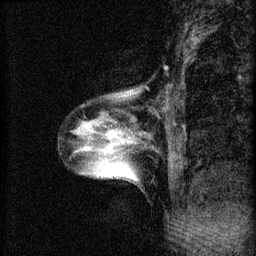
Breast MRI (dynamic contrast-enhanced), one sagittal slice. Position 14 of 60 along the scan axis. 3 images stored at this slice position (order not interpretable as contrast timing). 1.5 T. TE 4.2 ms, TR 8.2 ms. 2 mm slice thickness. 256 × 256 image matrix, field of view 180 × 180 mm. Patient: female, 40 years.
Annotated regions visible in this slice (semi-automatically segmented with operator editing):
- analysis volume of interest (the breast-tissue region the enhancement analysis was run in; not a lesion): bounding box <73,86,145,185> (left, top, right, bottom; pixels)
- tumour enhancement mask (voxels above the 70 % enhancement threshold inside the analysis volume of interest): <87,126,131,143>